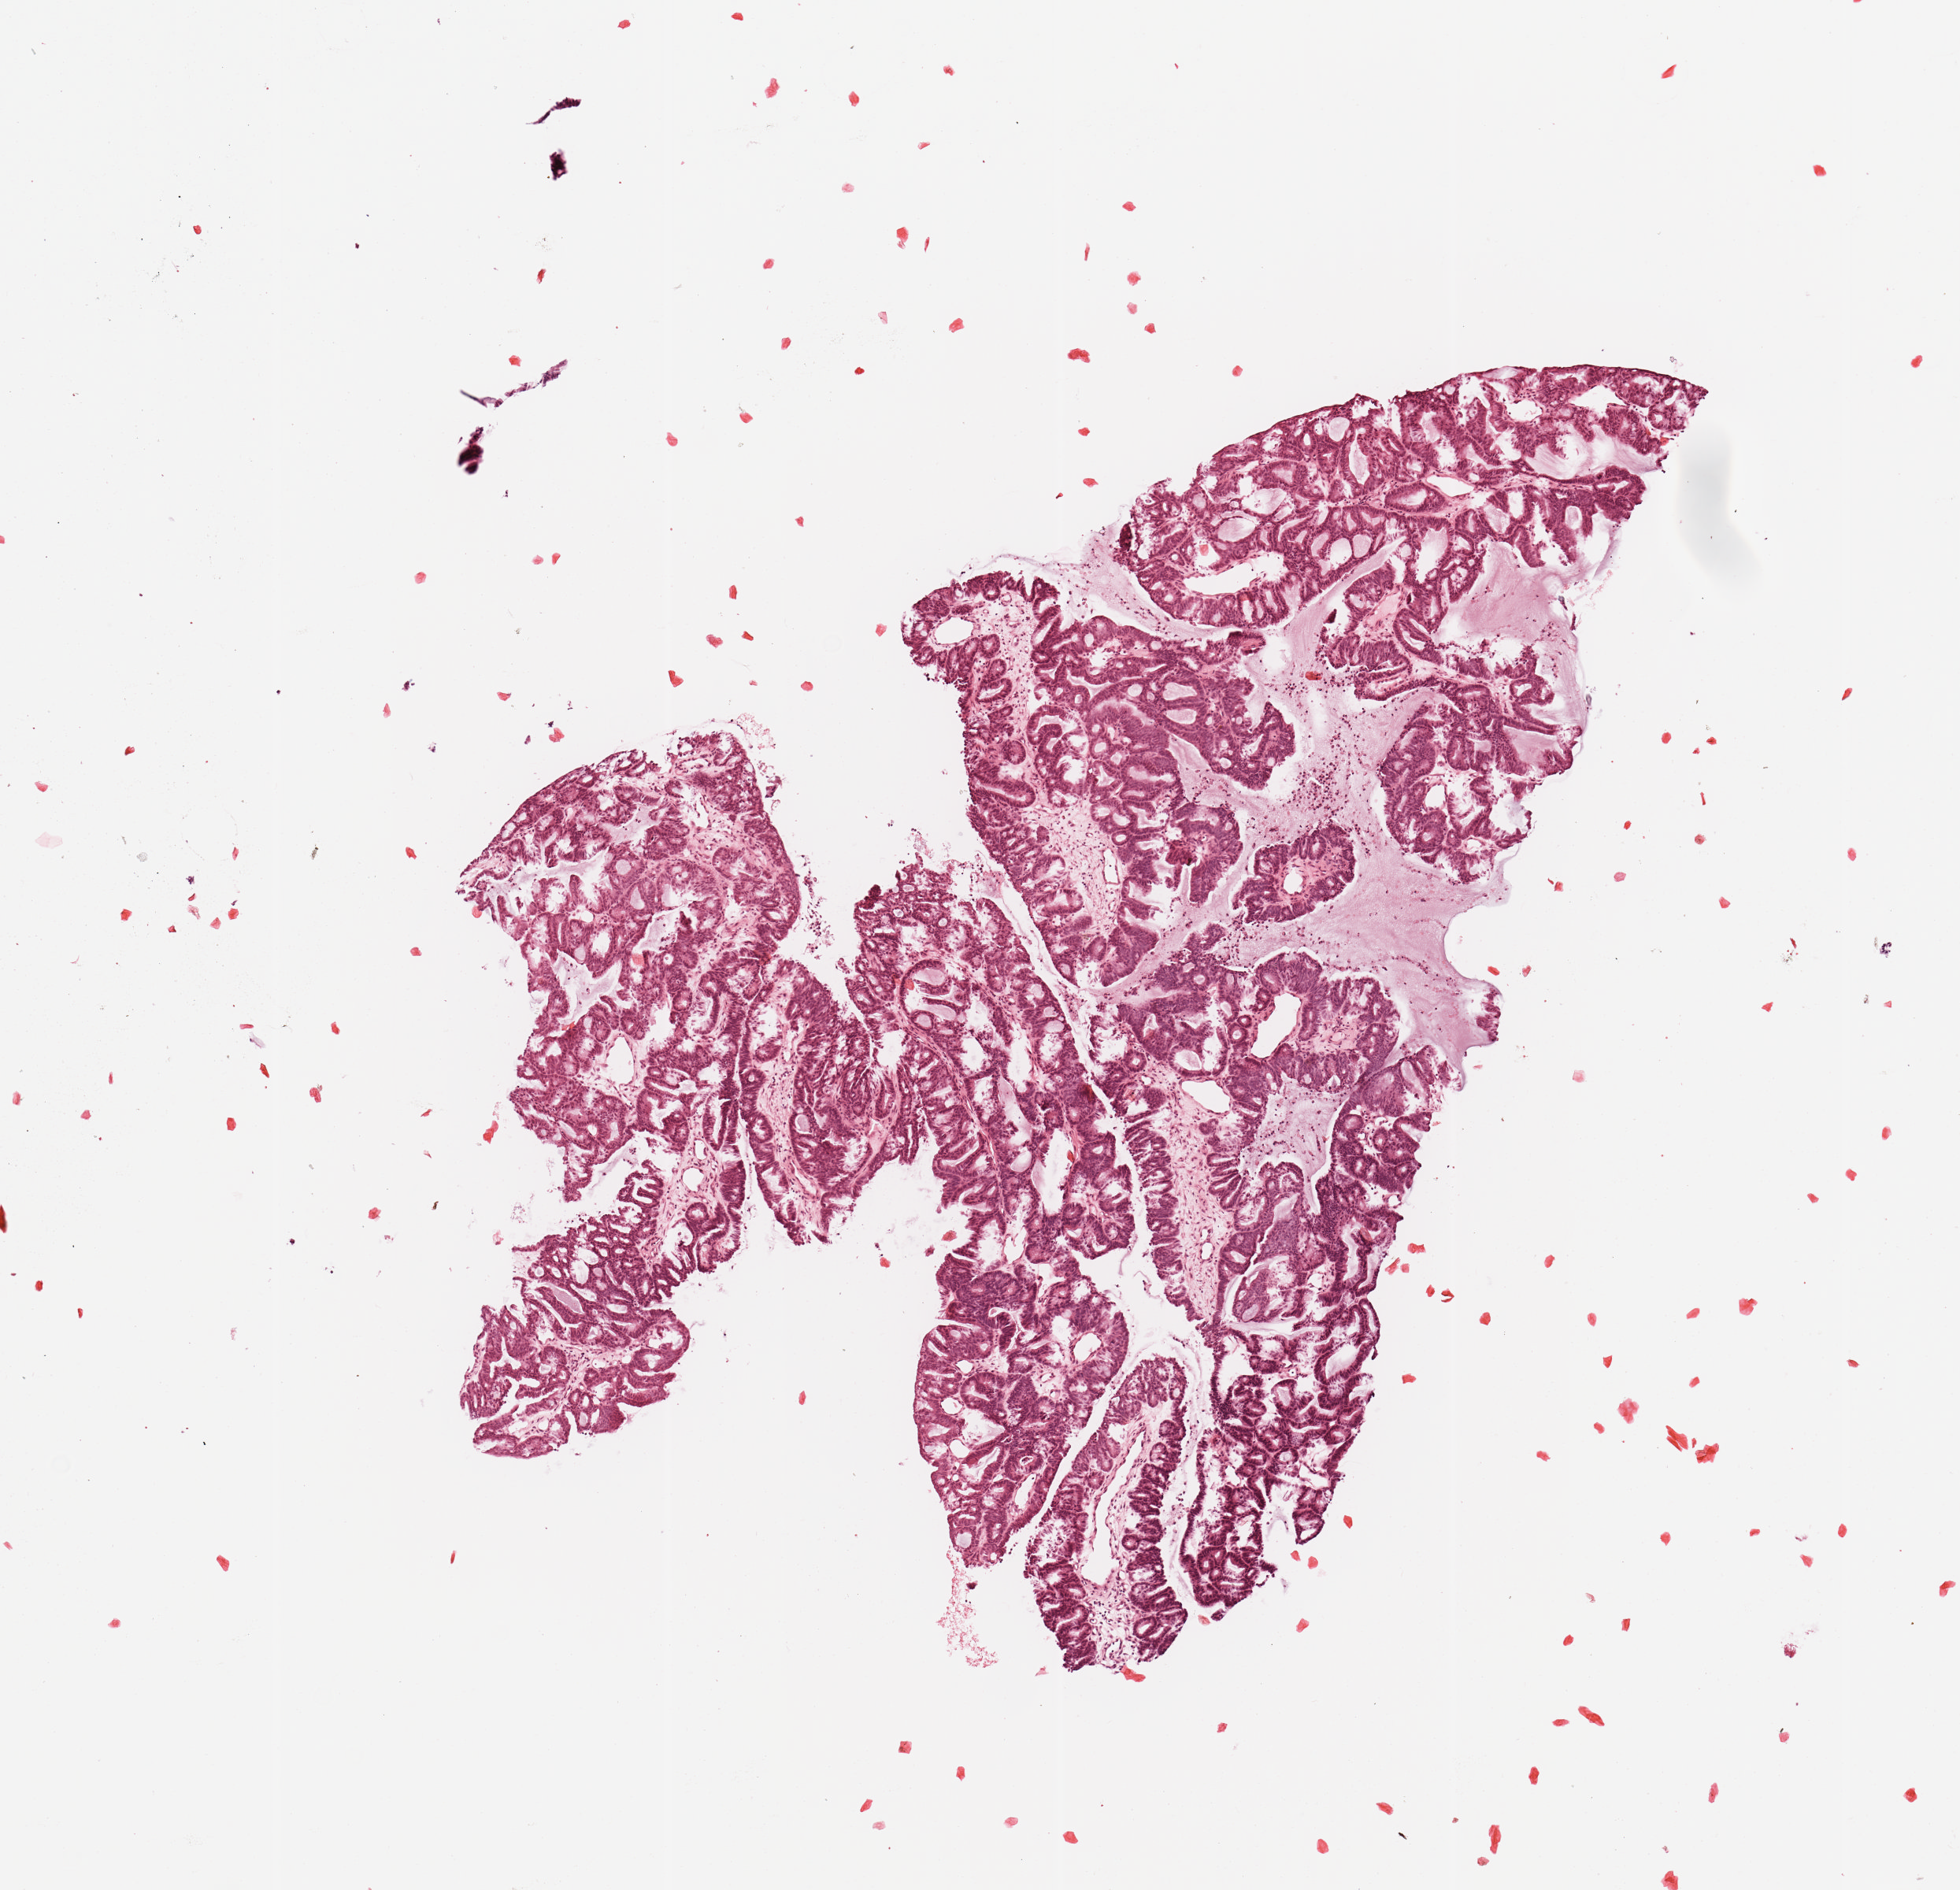
Digitized H&E-stained tissue section (whole slide) — shown as a low-resolution overview of the whole scanned area (about 4.9 x 4.7 mm, from a 20x scan). Uterus, tumour tissue. Female, 80 y/o. Histologic grade: G2 (moderately differentiated).
* primary tumour site (as recorded): posterior endometrium
* AJCC pathologic stage: I
* diagnosis: Endometrioid adenocarcinoma, NOS